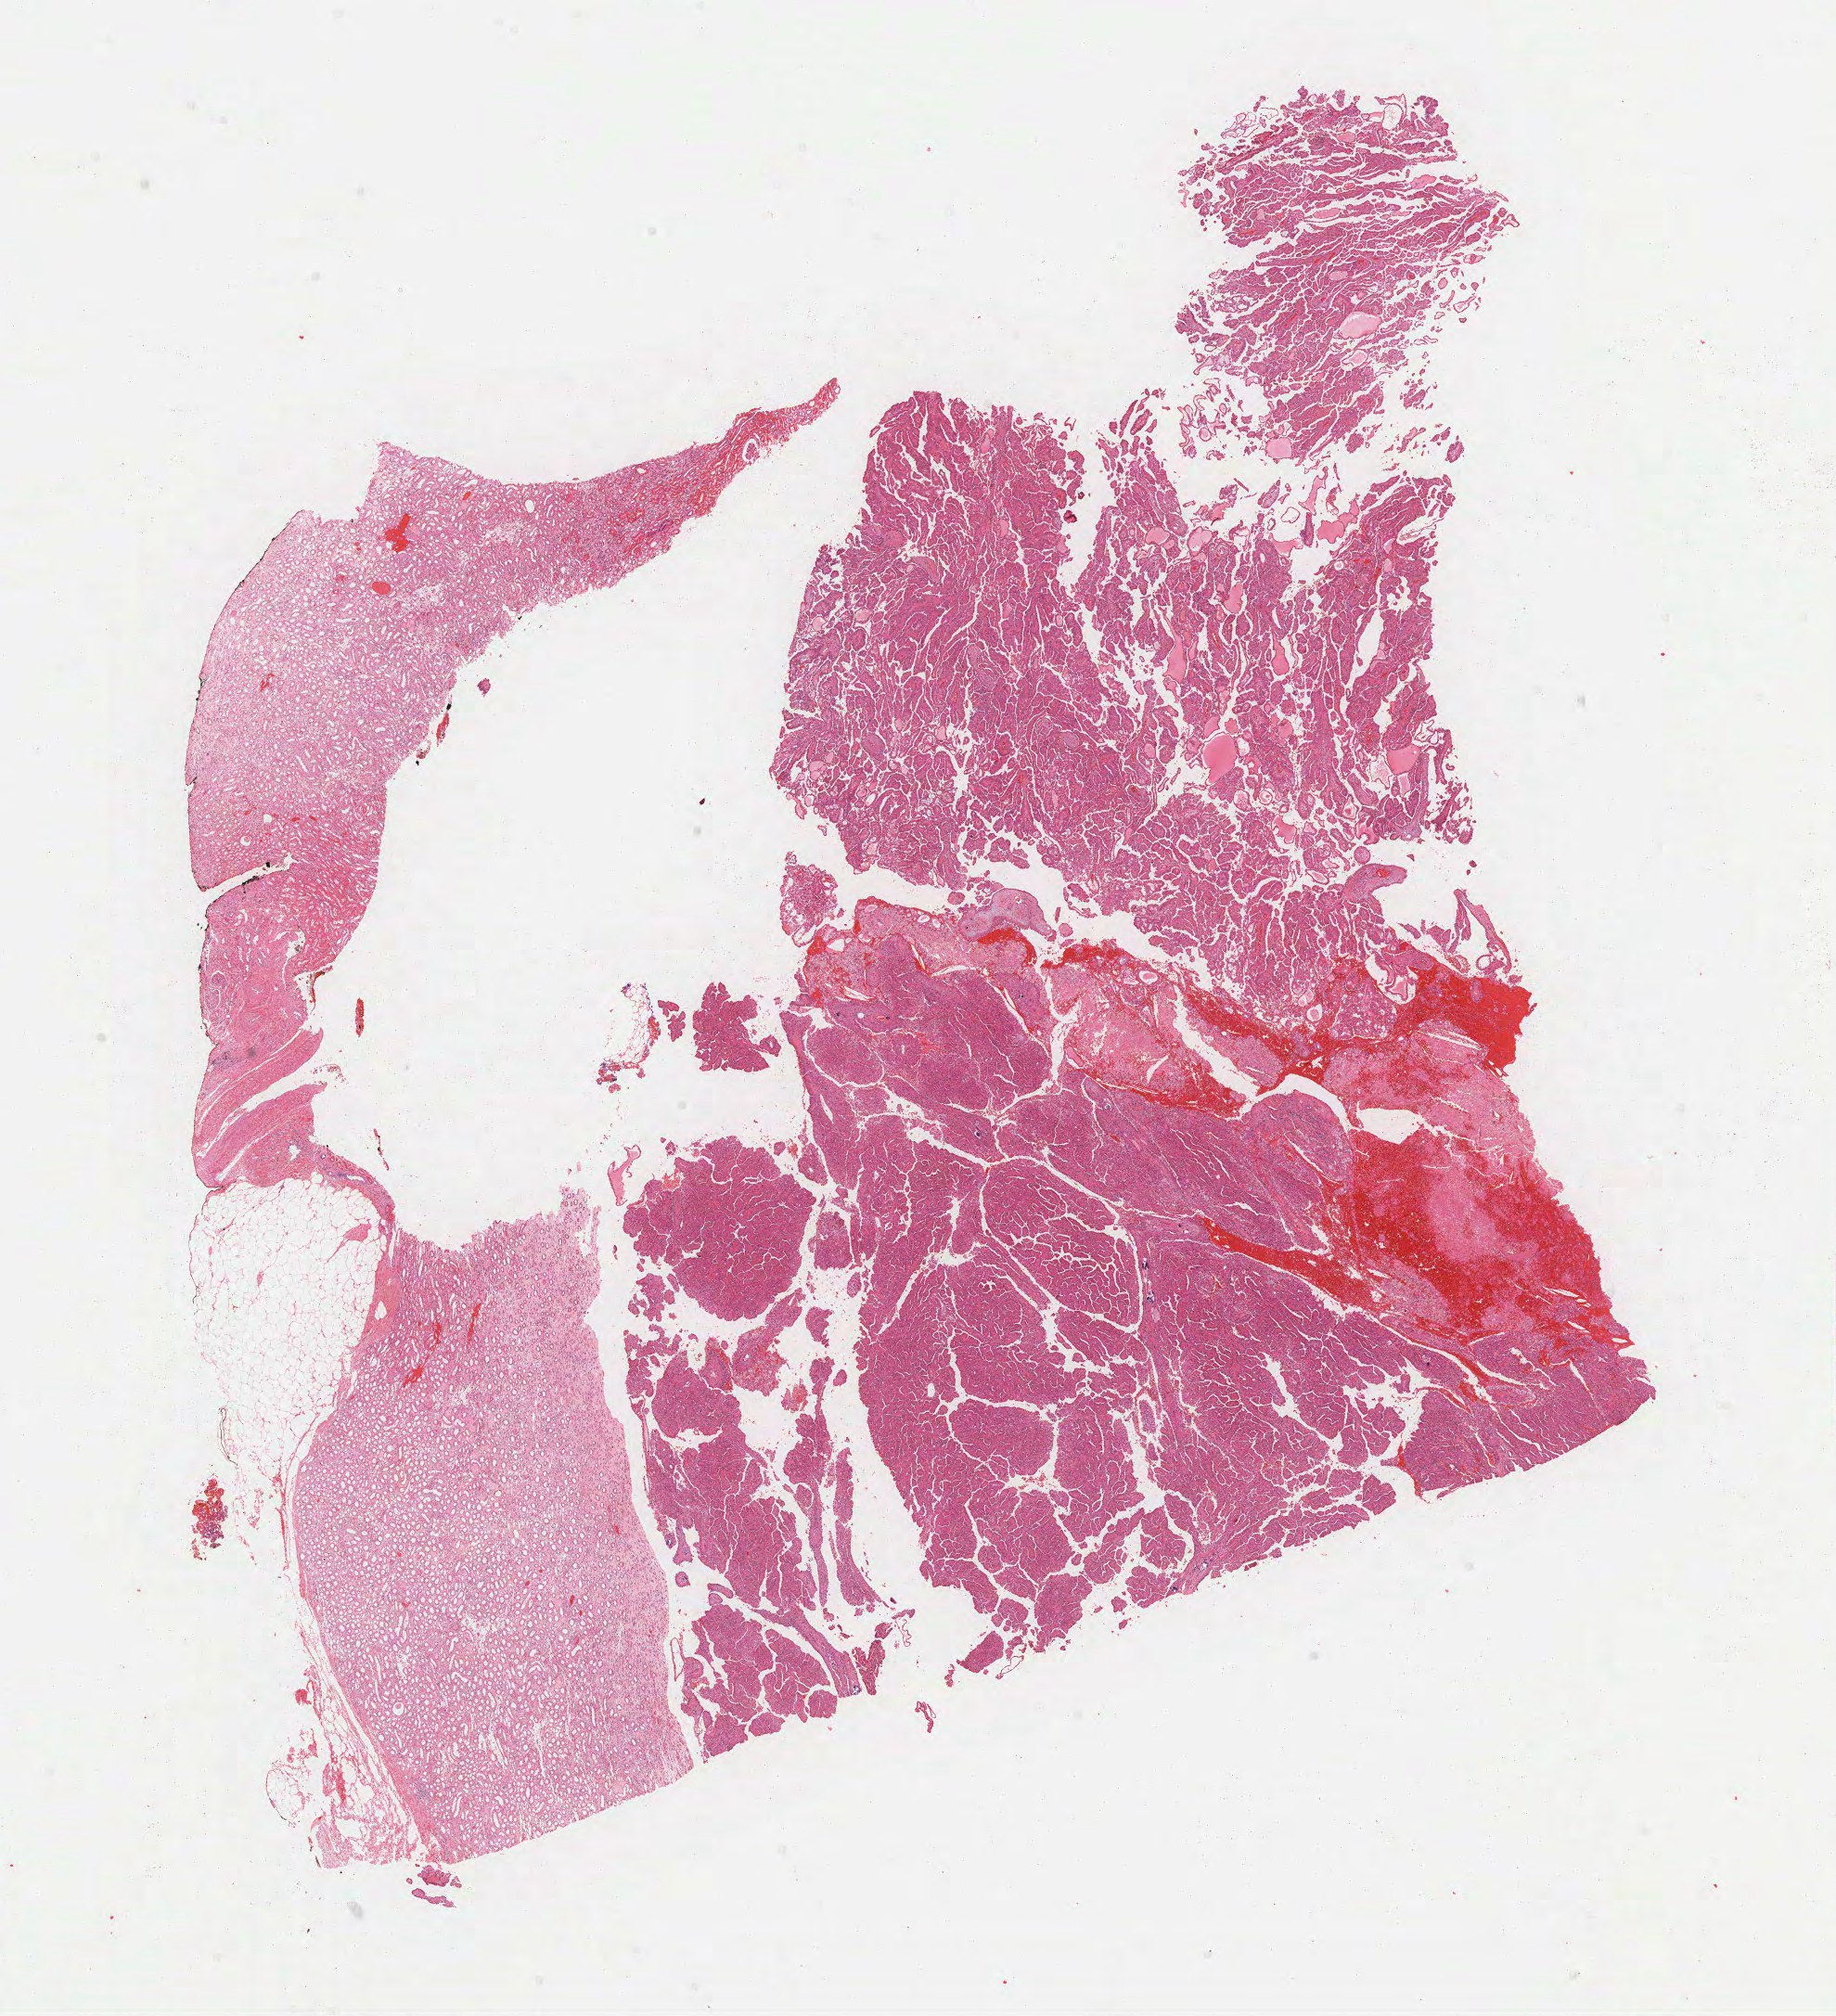
Digitized H&E tissue section (whole slide), whole scanned area (about 16.0 x 17.6 mm, slide scanned at 40x) shown as a low-resolution overview; formalin-fixed paraffin-embedded (FFPE) diagnostic section; primary tumour sample from the kidney. Male patient; age at initial diagnosis 50 years.
Laterality: left. Pathologic diagnosis: Papillary adenocarcinoma, NOS. AJCC pathologic stage: I (6th edition).